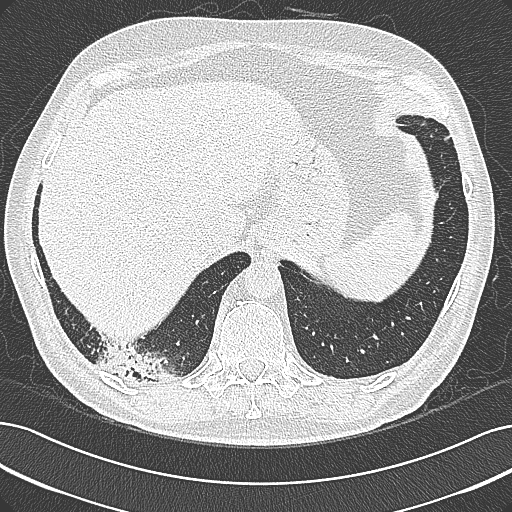
Chest CT (low-dose screening protocol), one axial image. Baseline screening round. Lung window (W 1500 / L -600 HU). 1 mm slice thickness. Lung (sharp) reconstruction kernel (B80f). Slice 253 of 355 in the series. 512 × 512 image matrix. Male, age 68 years at enrolment. Former smoker at enrolment.
Lesion marked by an expert reader, bounding box (x1, y1, x2, y2) in pixels: (94, 337, 193, 398). Screening reader's record for this exam: no non-calcified nodule ≥4 mm recorded. Official screen result: negative screen, significant abnormalities not suspicious for lung cancer. Participant outcome: lung cancer diagnosed 154 days after this screen — mucinous adenocarcinoma, right lower lobe, well differentiated (G1), stage IB (AJCC 6th edition), 50 mm at pathology.